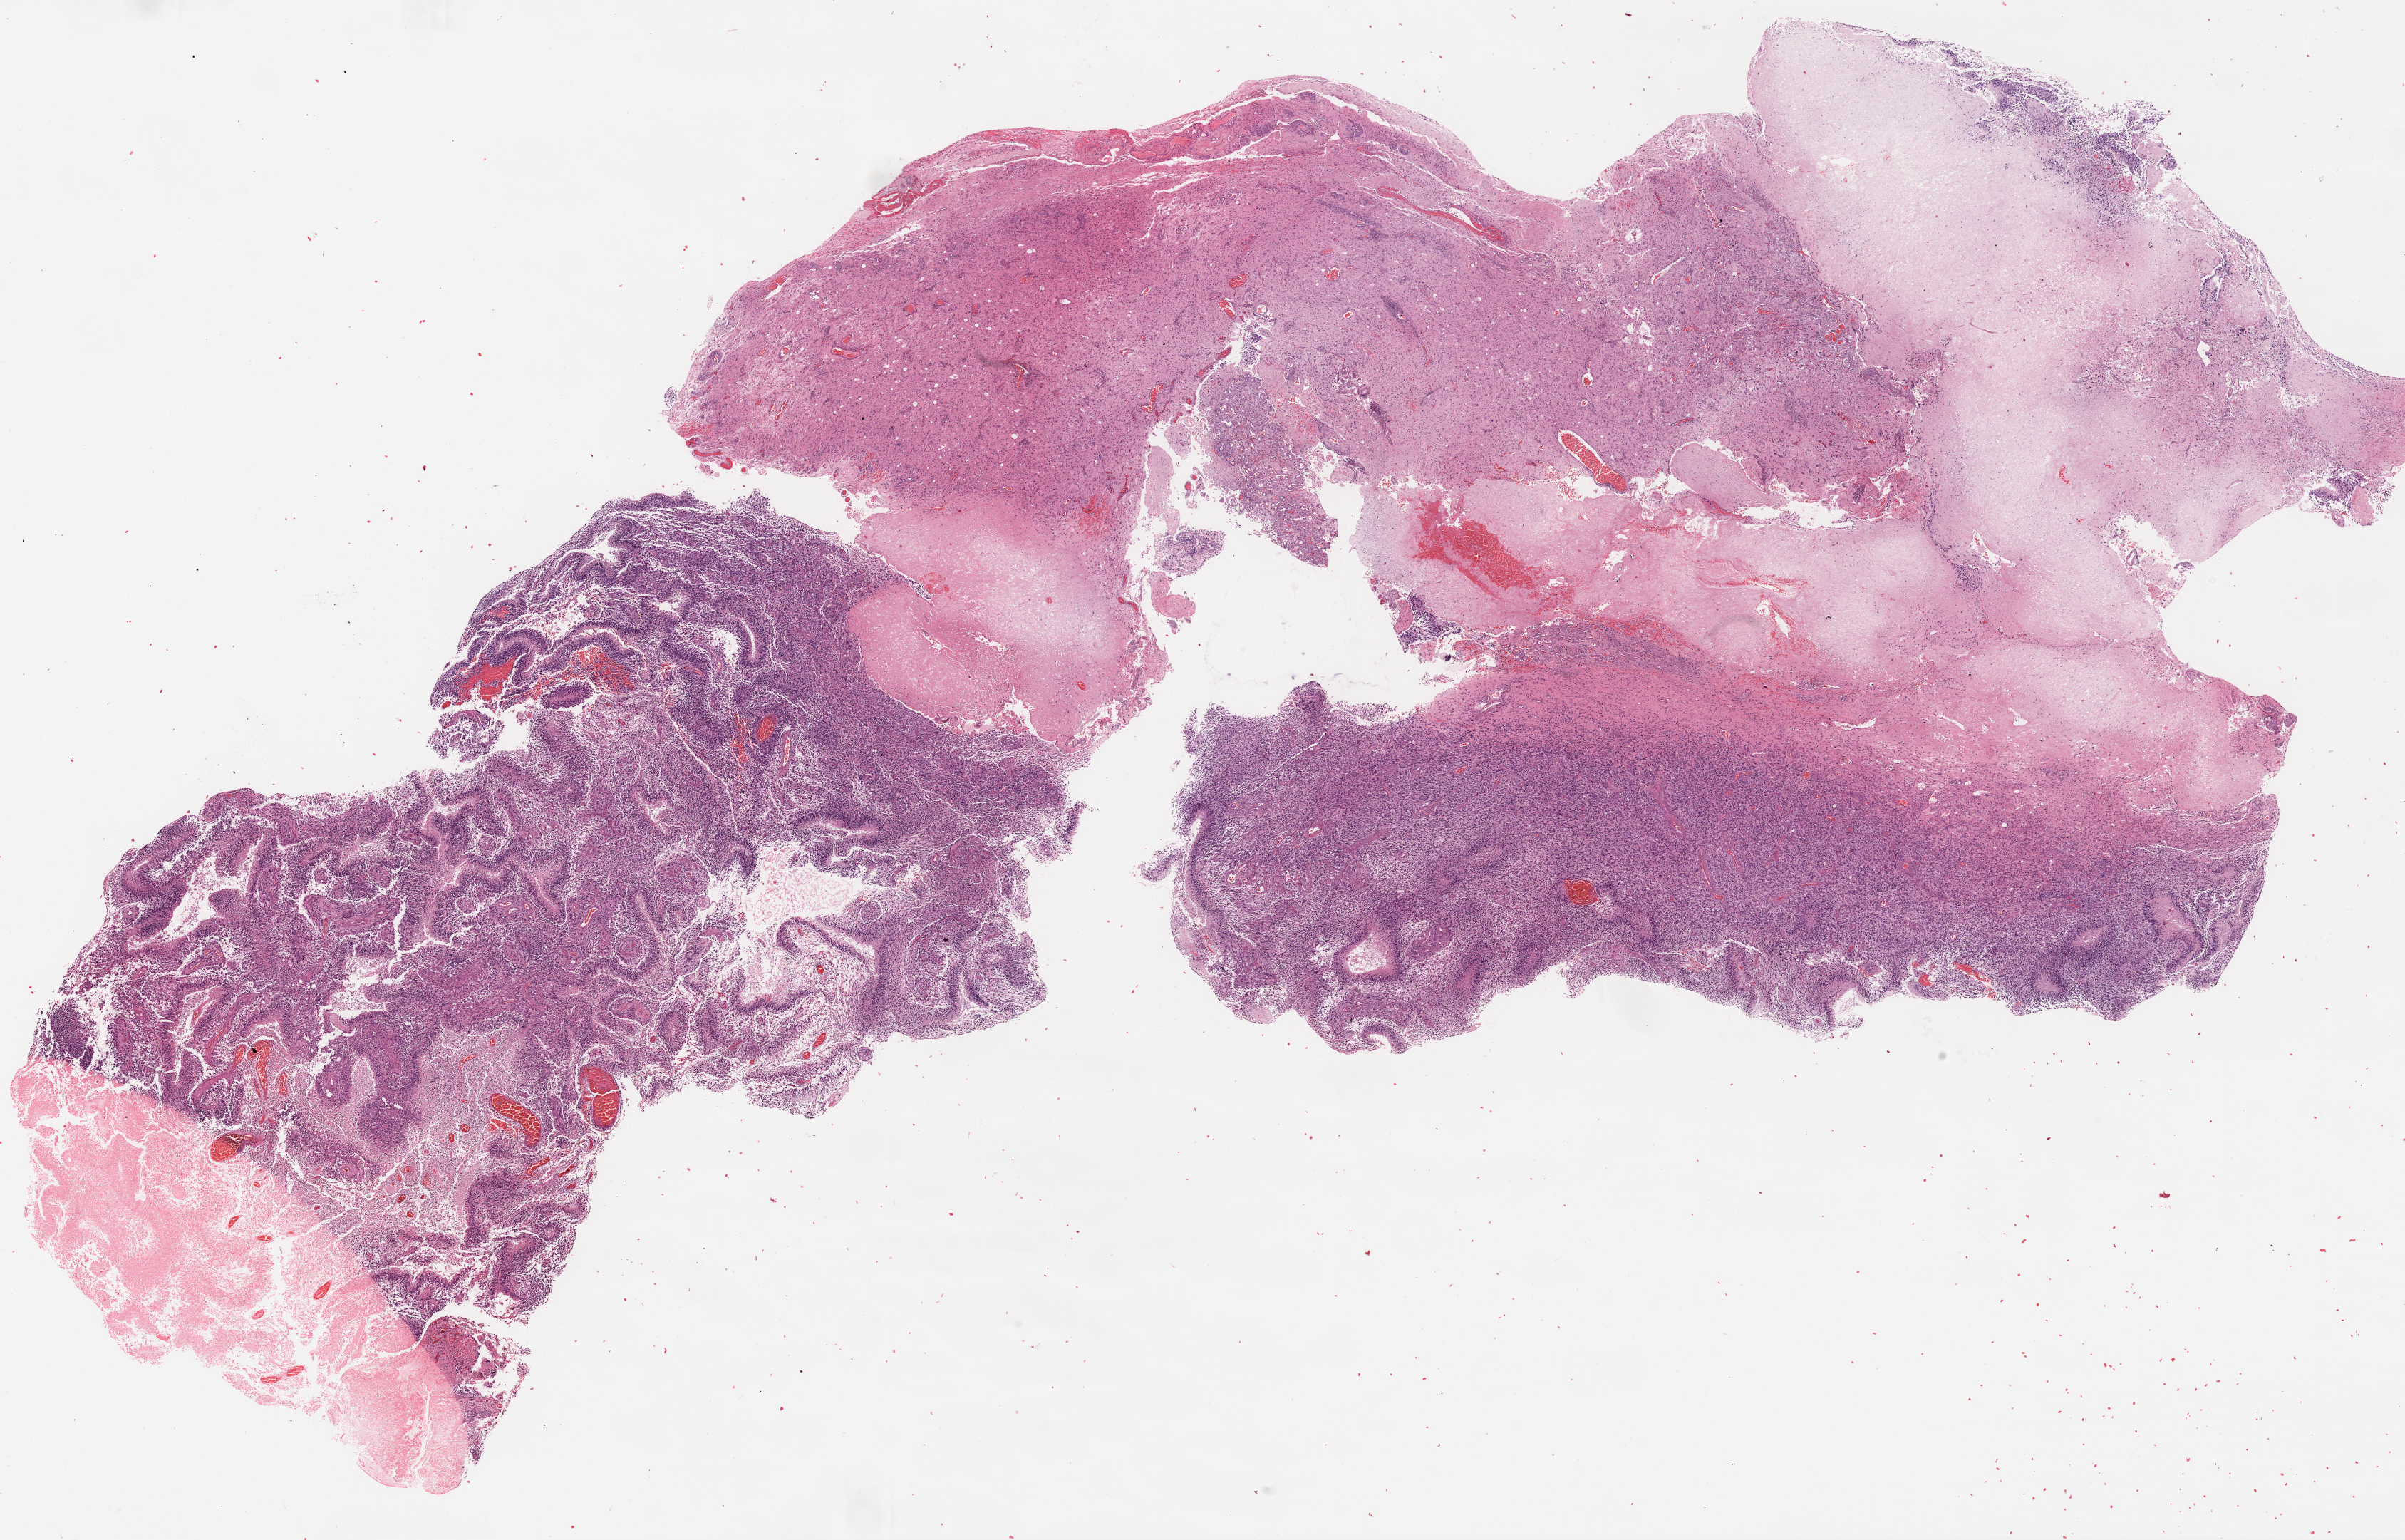
Digitized H&E-stained tissue section (whole slide), a low-resolution overview of the entire scanned area, about 27.1 x 17.3 mm, formalin-fixed paraffin-embedded (FFPE) diagnostic section, sample: primary tumour, brain. Male, age 50 years at initial diagnosis.
• pathologic diagnosis: Glioblastoma